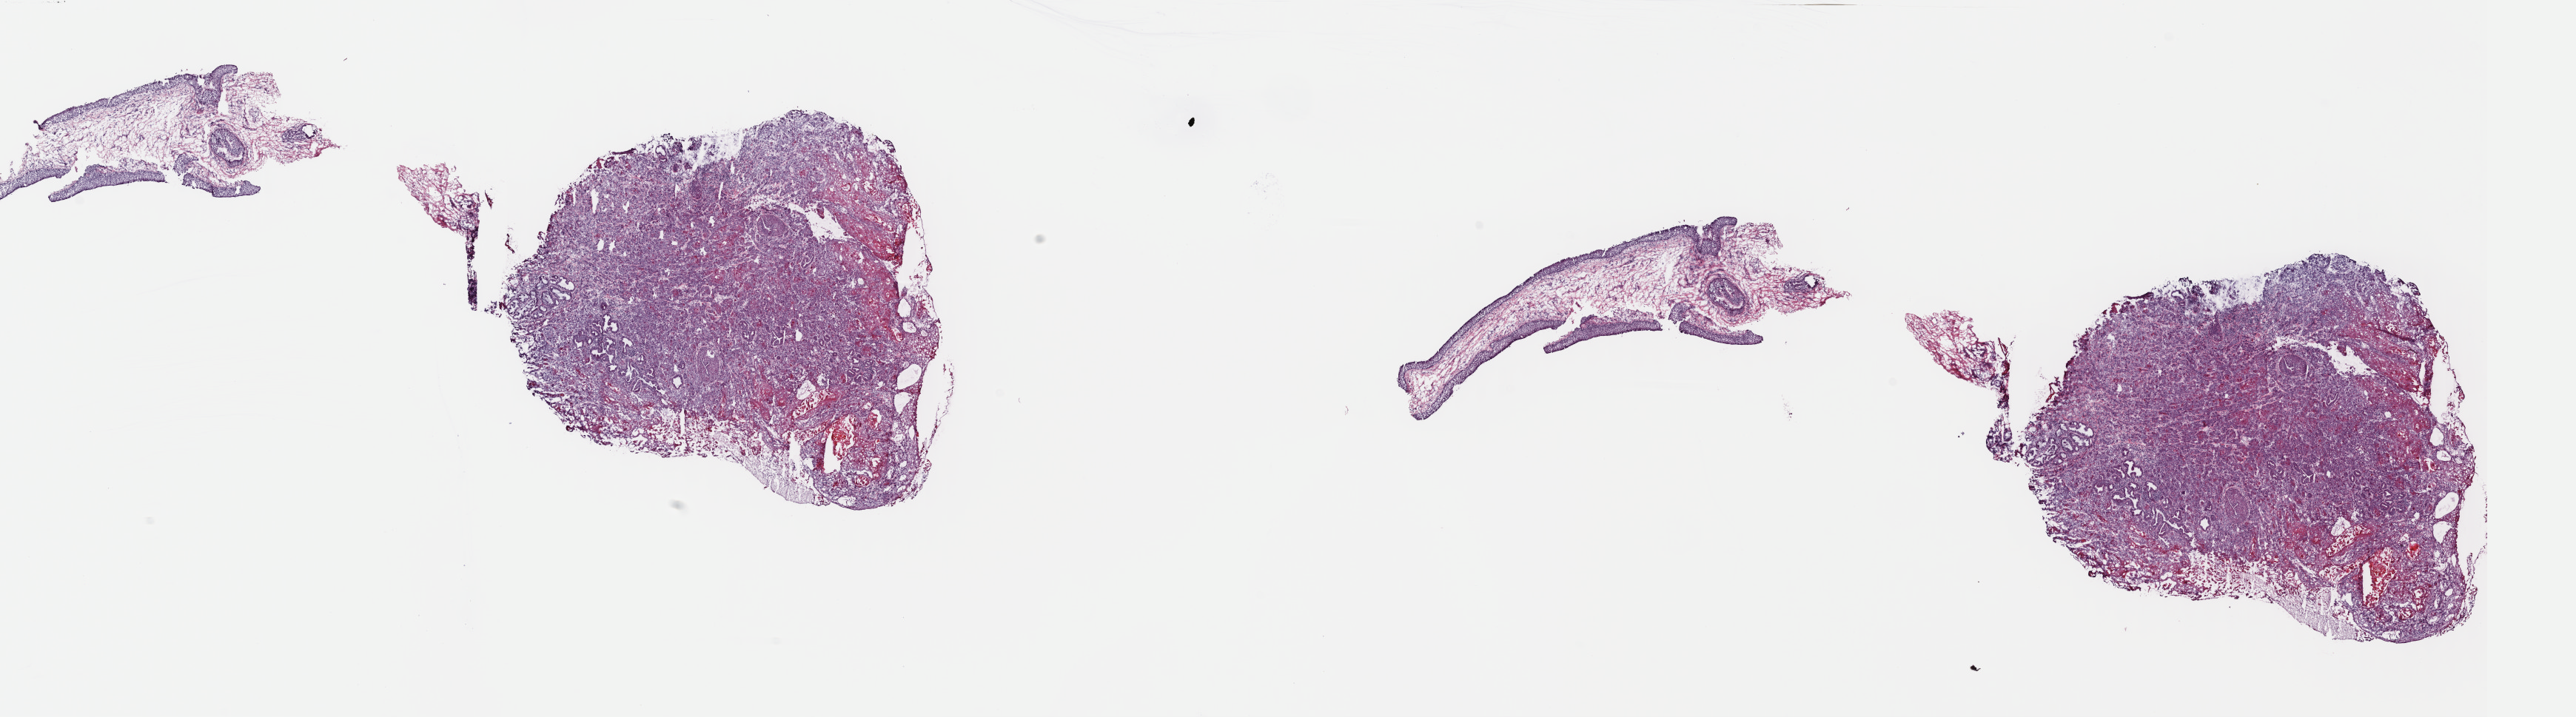
Digitized H&E tissue section (whole slide) — shown as a low-resolution overview of the whole scanned area (about 27.4 x 7.6 mm), frozen section from the top of the tissue portion, head and neck, primary tumour sample. Male patient; age at initial diagnosis 62 years. Histologic grade: G2 (moderately differentiated). Composition of this section per pathologist review: tumour cells 85%, tumour nuclei 75%, normal cells 15%, stromal cells 0%, necrosis 0%. Infiltration values recorded for this section: lymphocyte infiltration 3%, monocyte infiltration 0%, neutrophil infiltration 1%.
Laterality: left. Diagnosis: Squamous cell carcinoma, keratinizing, NOS.